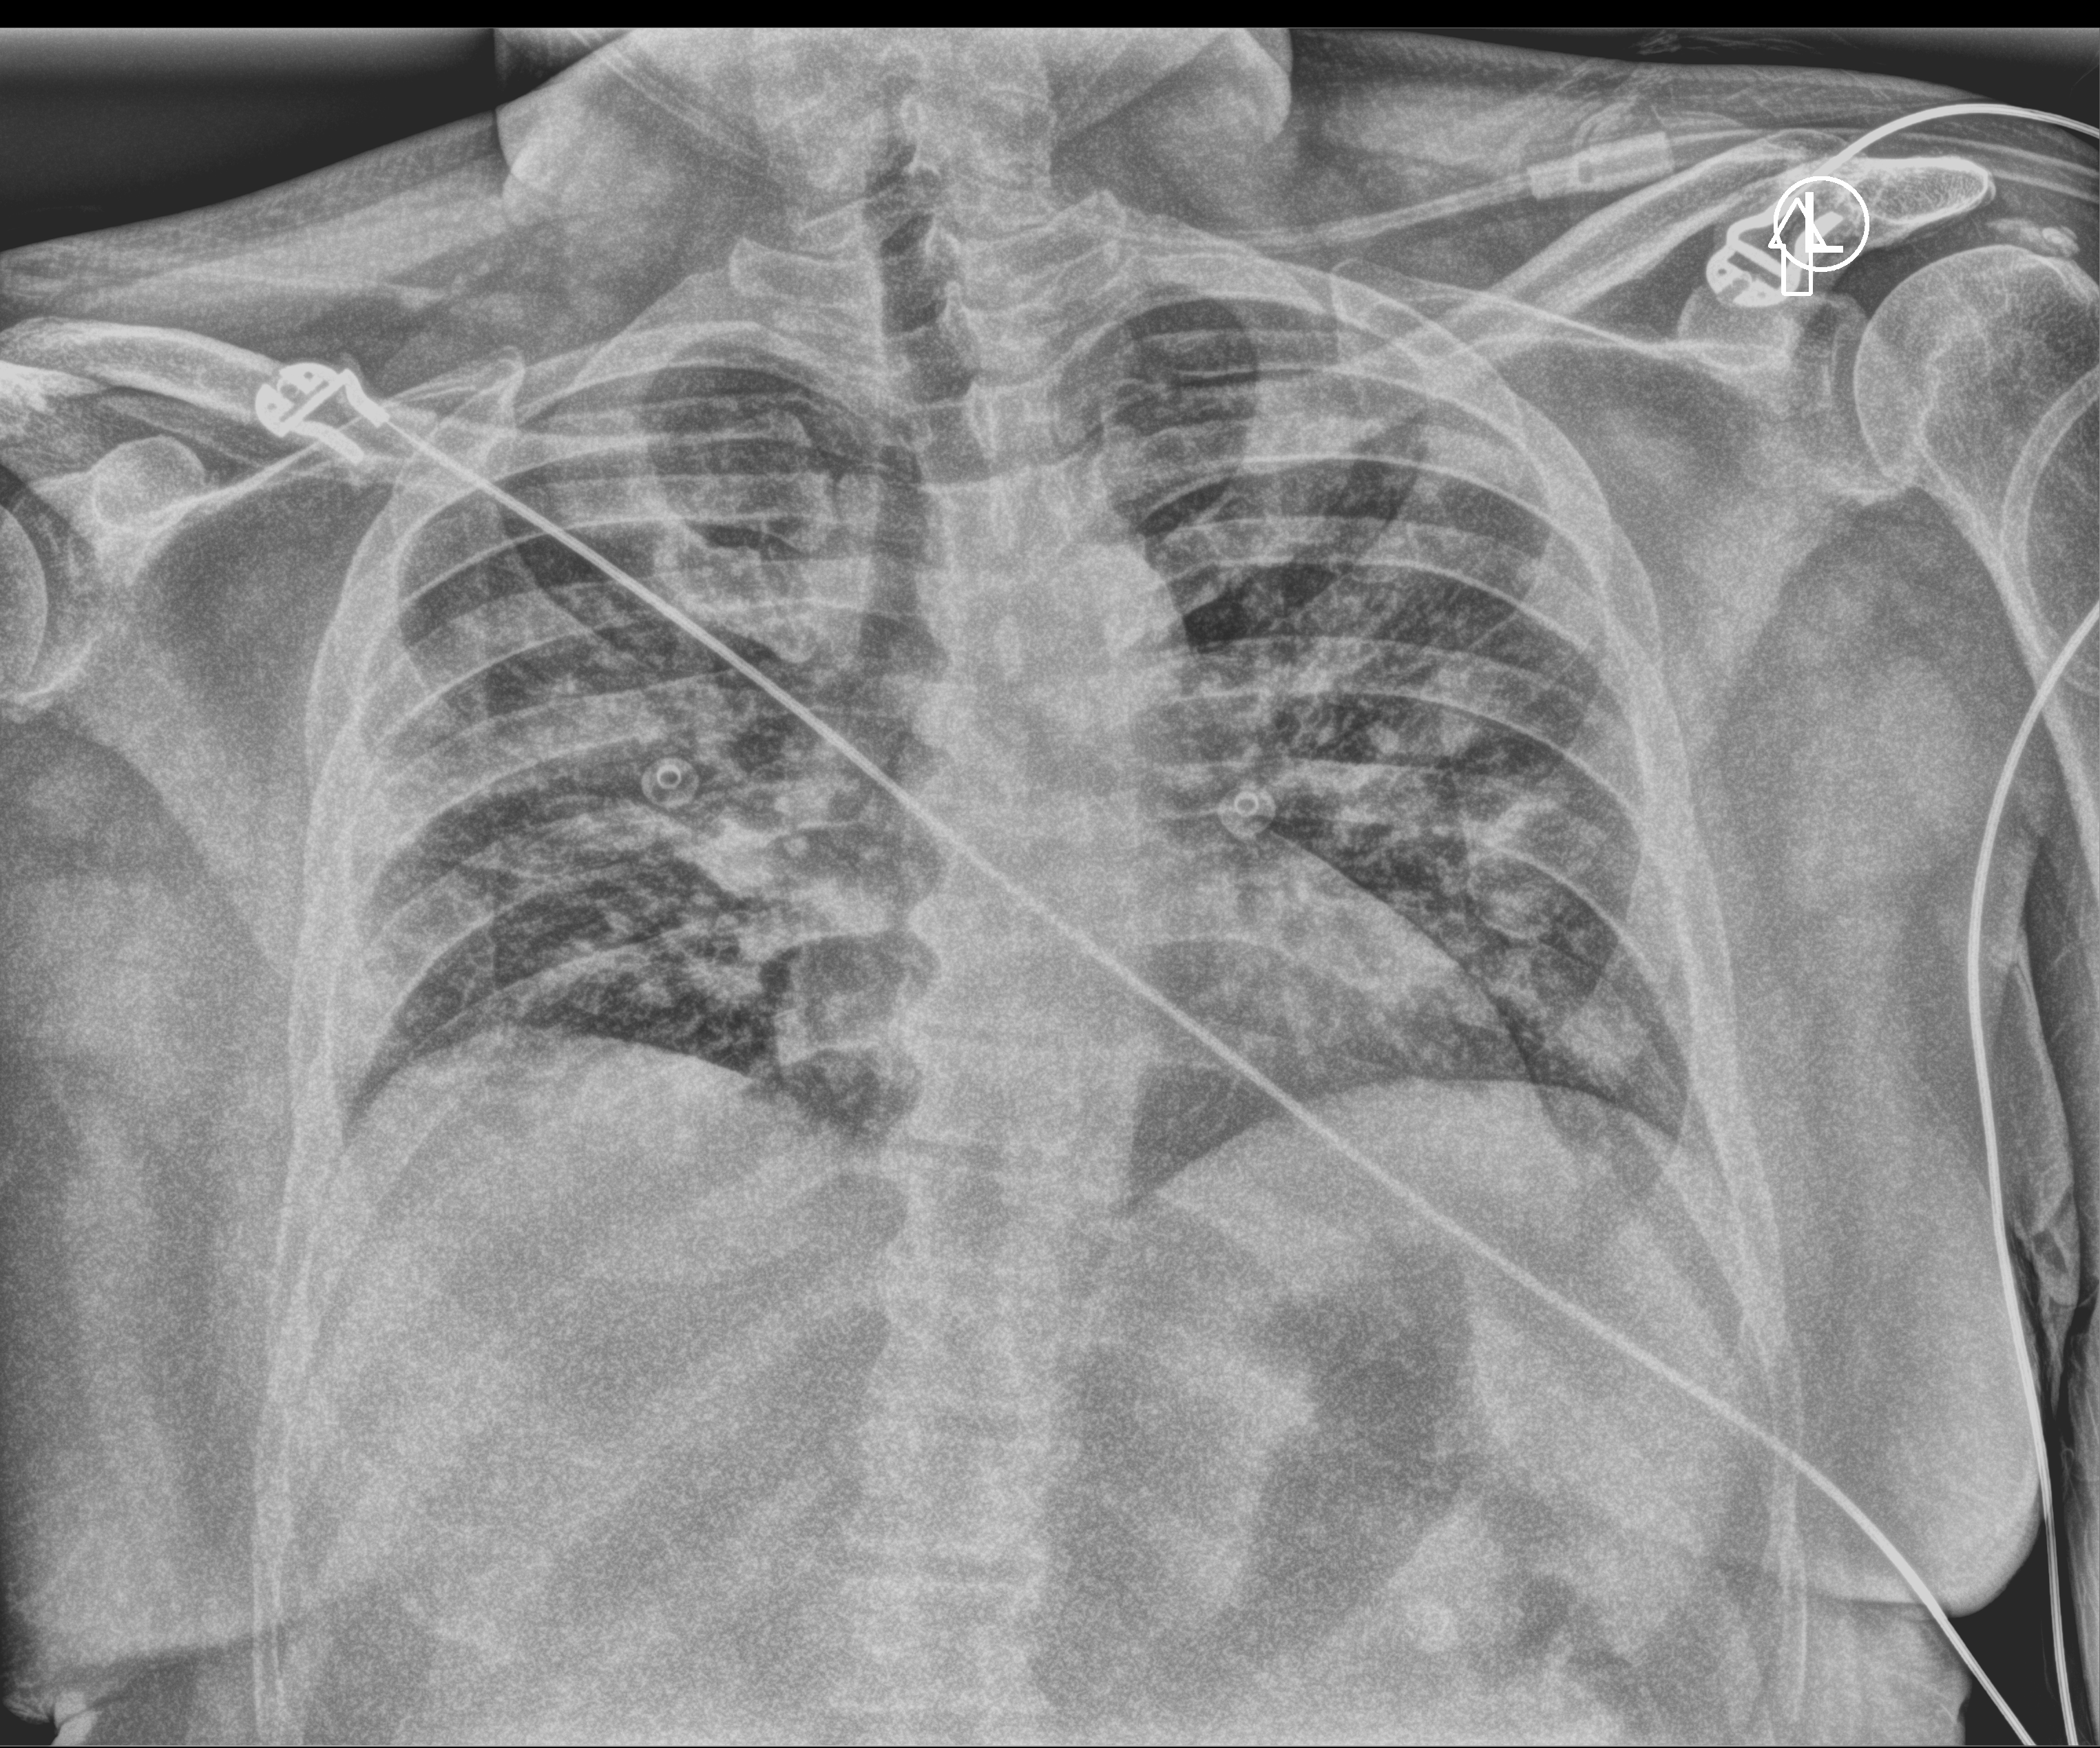
Portable chest radiograph, anteroposterior (AP) projection. Patient hospitalised with COVID-19; male, aged 60–74 years.
Admission-level facts for this patient (not findings on this image; timing relative to this image not recorded):
- admitted to intensive care during this hospital stay: no